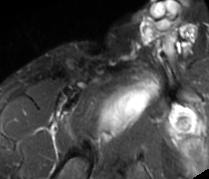
MRI of an extremity soft-tissue mass, one axial slice; slice 74 of 89 in the series (ordered by position); STIR; MR volume resampled by the dataset authors to the PET/CT grid (not the native acquisition matrix); 3.27 mm slice thickness; 209 × 179 image matrix, field of view 204 × 175 mm. Male patient. From the clinical record (not read from this slice): histological type: undifferentiated - pleiomorphic; grade: high; site of the primary tumour: right thigh.
Outlined on this slice (expert contour drawn on MRI and transferred to this co-registered scan by the dataset authors):
- gross tumour volume including surrounding oedema: bounding box [x1, y1, x2, y2] px = [98, 75, 161, 141]
- gross tumour volume (mass): [98, 82, 156, 136]